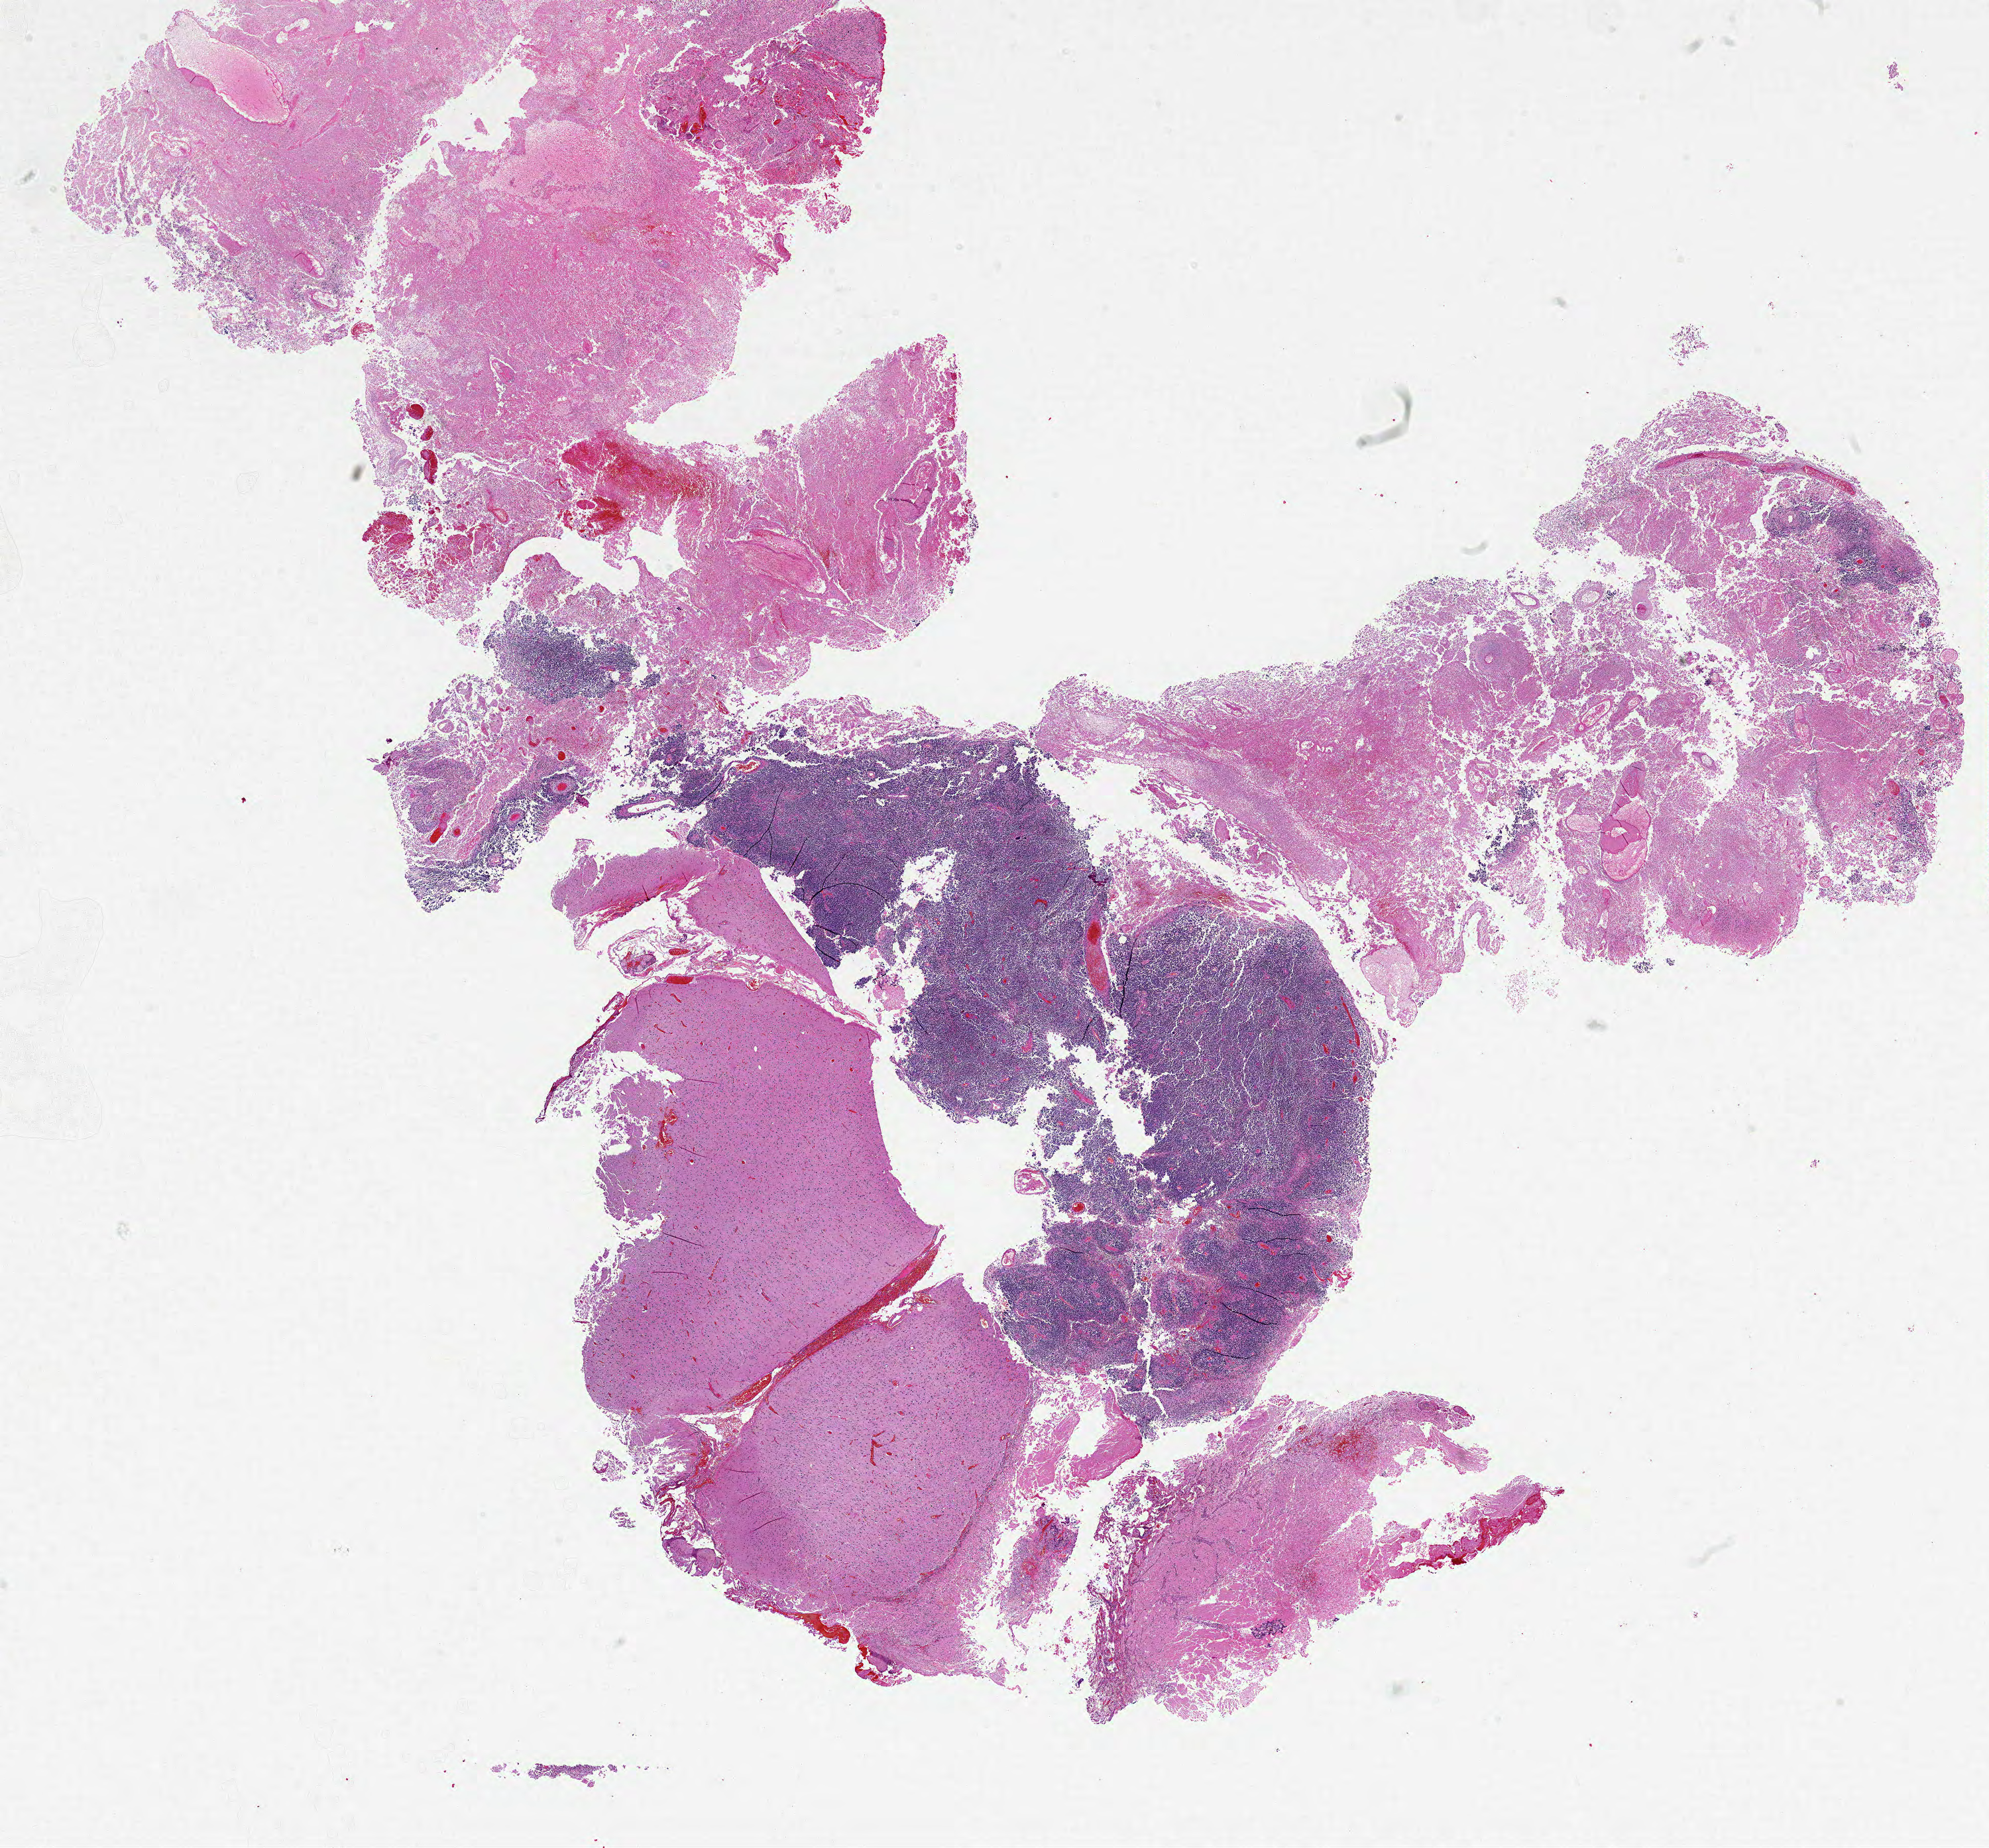
Whole-slide histology image, Hematoxylin and eosin (H&E) stained, low-resolution overview of the scanned area, about 24.0 x 22.3 mm; formalin-fixed paraffin-embedded (FFPE) diagnostic section; primary tumour sample from the brain. Patient: male, age at initial diagnosis 46 years.
Diagnosis: Glioblastoma.